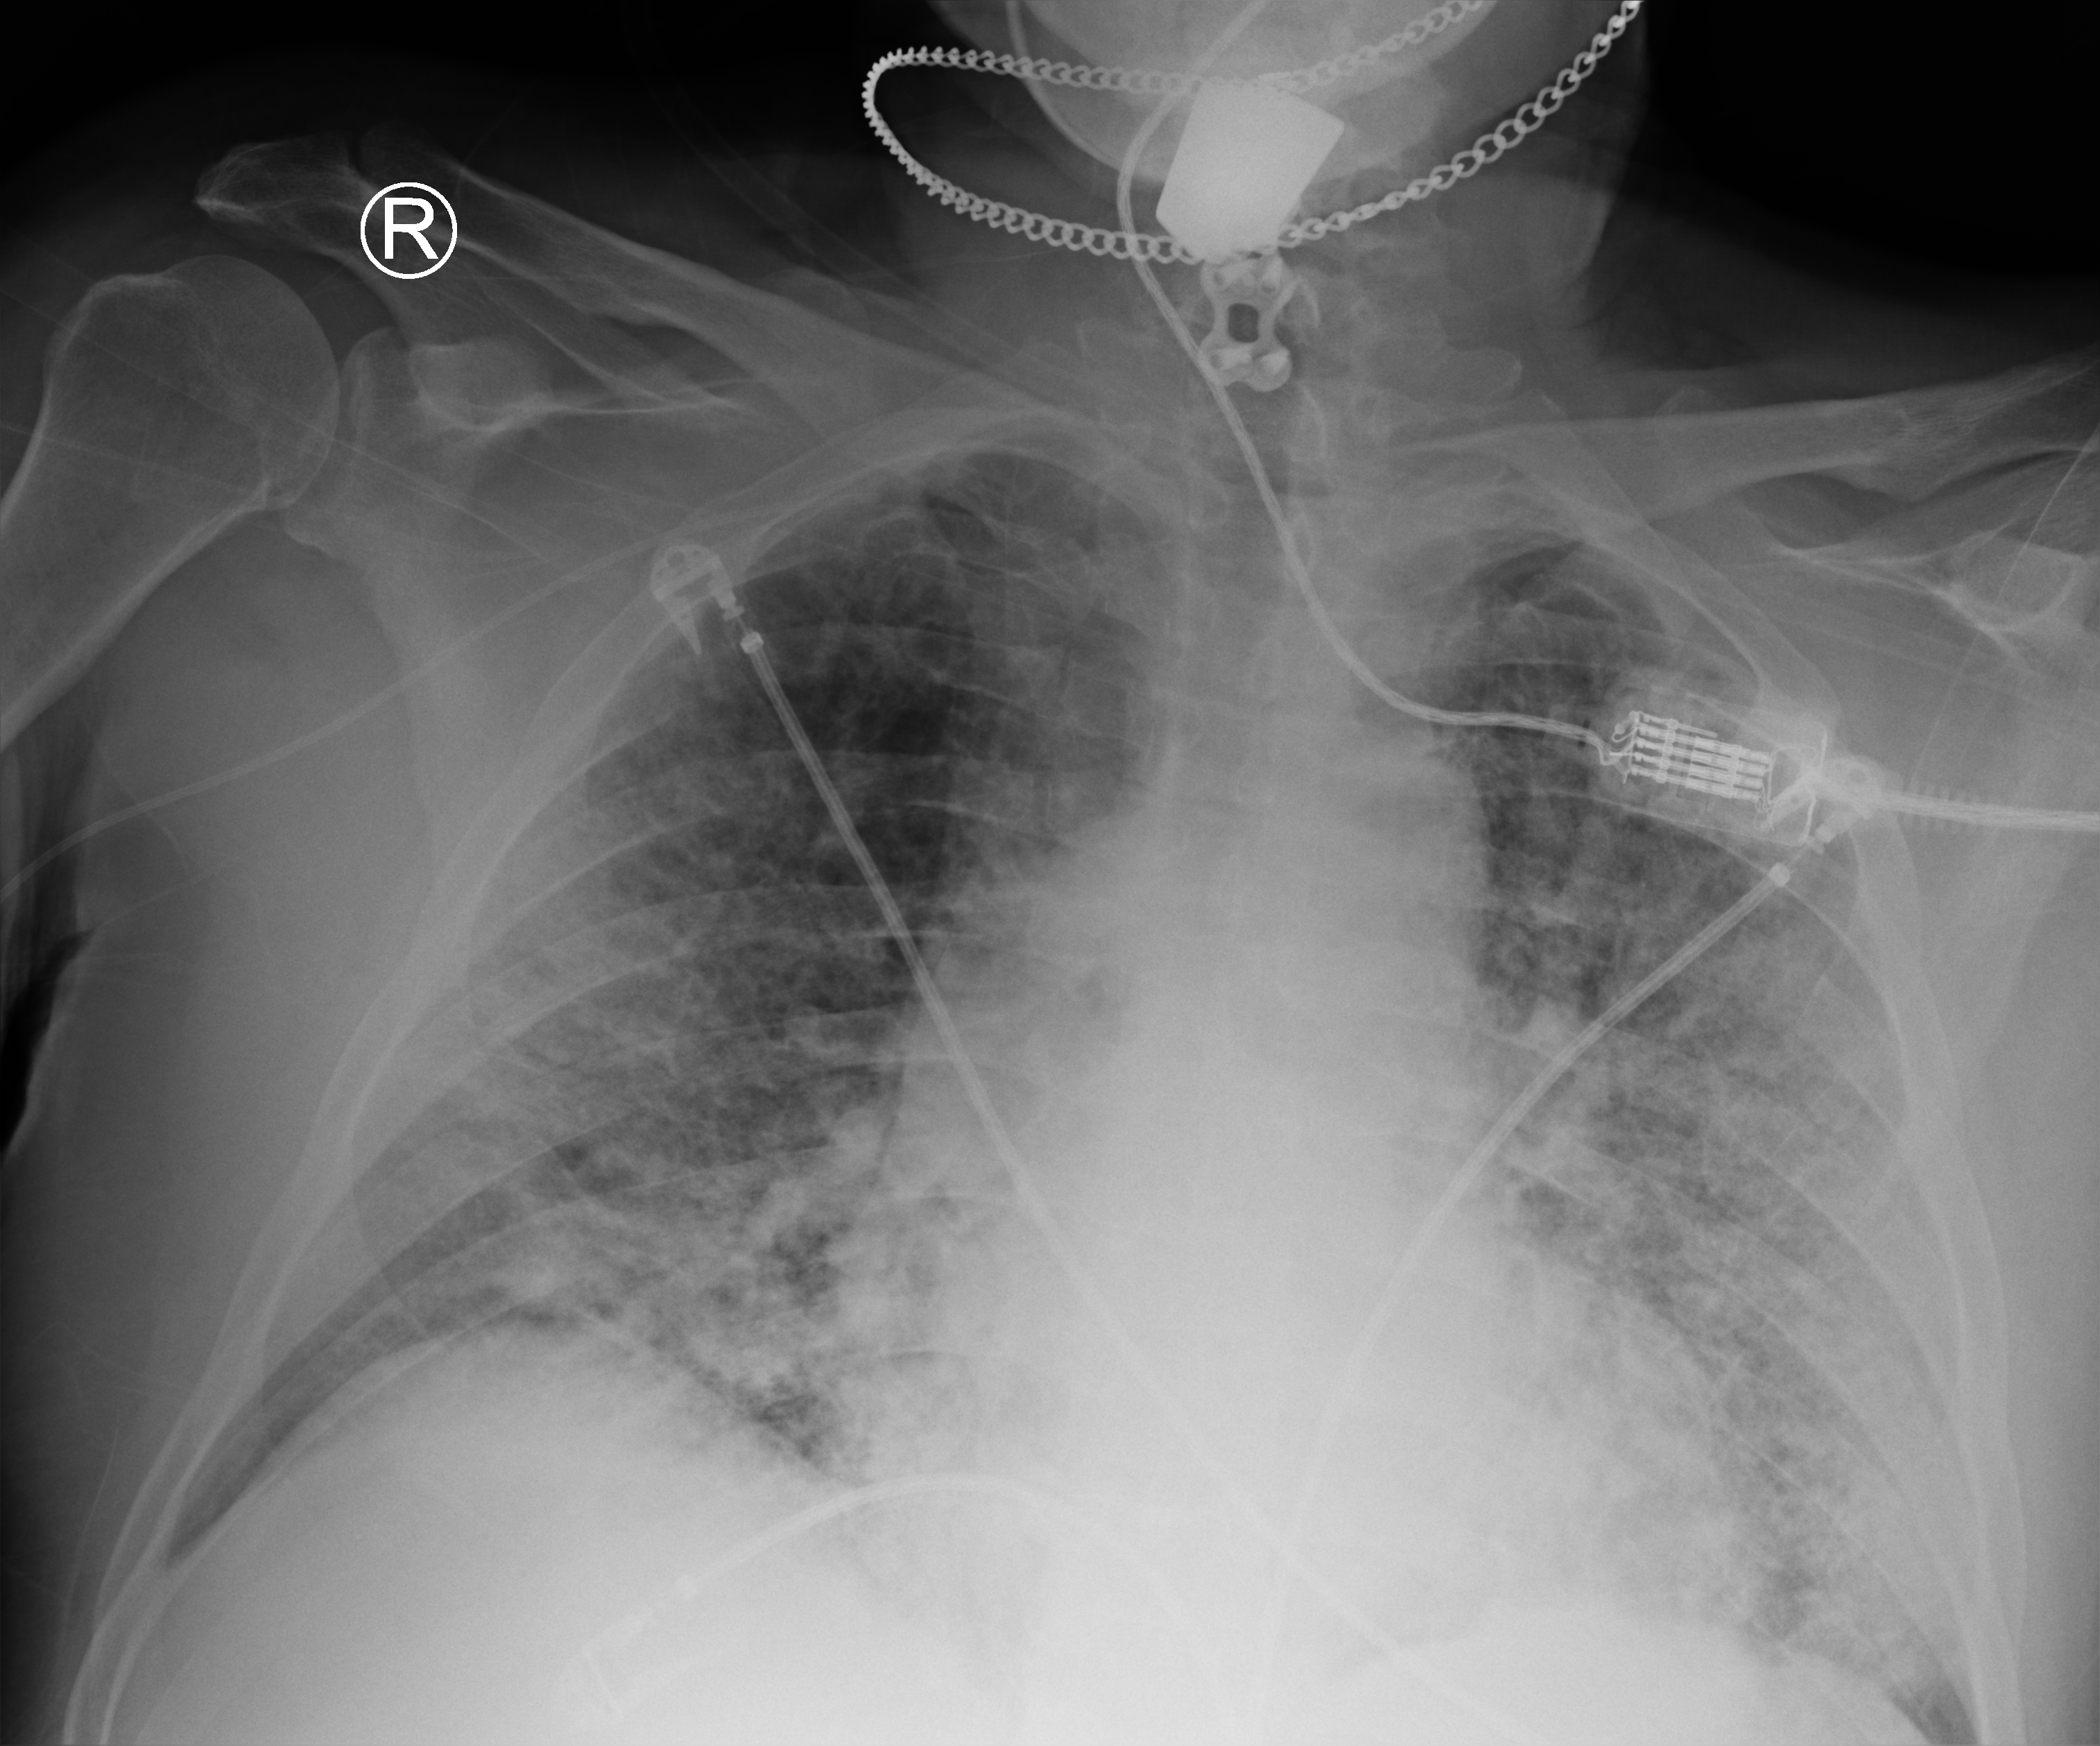
Chest X-ray (portable), anteroposterior (AP) projection. Patient hospitalised with COVID-19; male, aged 60–74 years.
From the hospital-stay record, not from the radiograph (when in the stay this image was taken is not recorded): admitted to intensive care during this hospital stay: no.